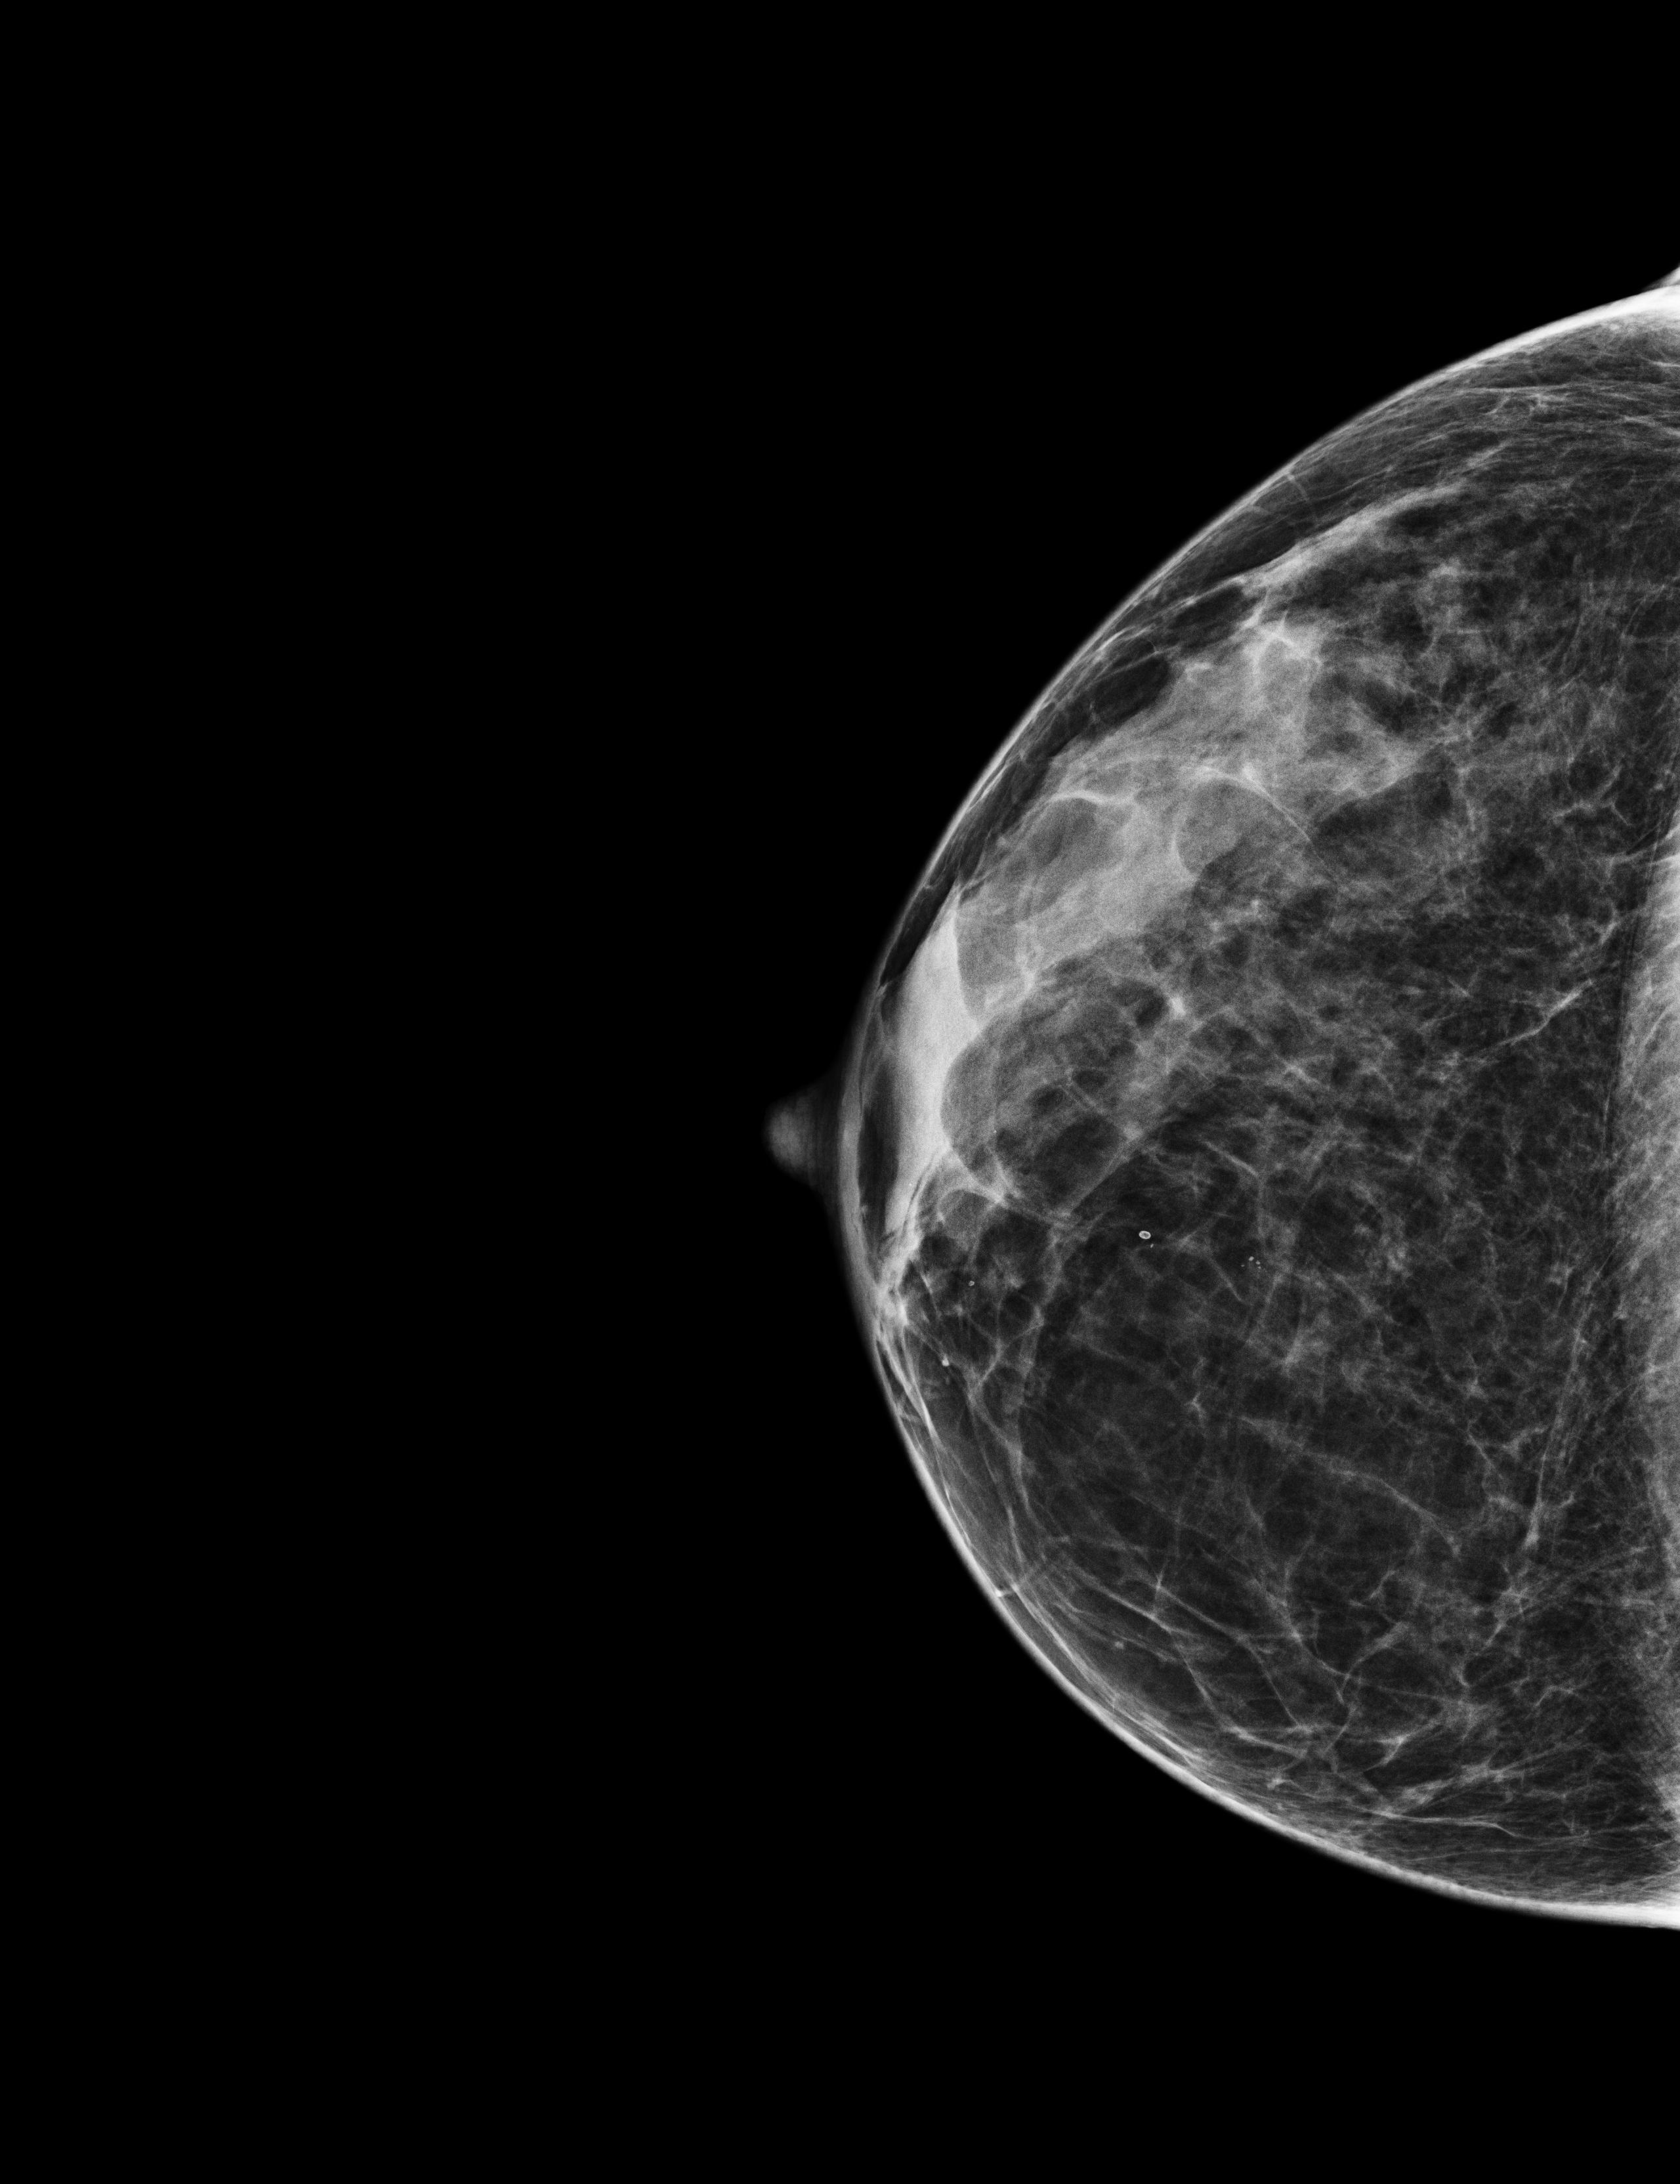
Screening examination, compressed breast thickness 43 mm. Patient aged 47 years (female).
Image type: full-field digital mammogram. Breast: right. Projection: craniocaudal (CC) view.